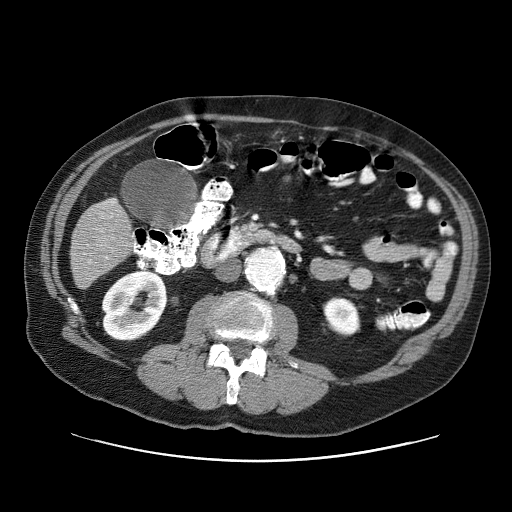
Contrast-enhanced abdominal CT (liver protocol), one axial slice; slice 11 of 87 in the series (ordered by position); reconstruction kernel STANDARD; 120 kVp; one of 3 acquisitions stored at this slice position; soft-tissue window (W 400 / L 40 HU); 2.5 mm slice thickness; 512 × 512 image matrix, field of view 400 × 400 mm. Case-level facts recorded for this patient, not image findings: diagnosis: hepatocellular carcinoma (patient treated with transarterial chemoembolisation; whether this scan precedes or follows treatment is not stated here); TNM stage (as recorded): Stage-IIIA; Child-Pugh class: A; tumour differentiation: well differentiated.
Structures marked on this image (semi-automatically segmented with operator editing):
- liver parenchyma outside the tumour (the mass and vessels are separate outlines, so this box may not span the whole liver): bounding box (x1, y1, x2, y2) in pixels: (70, 198, 133, 288)
- liver vessels: (109, 200, 115, 205)